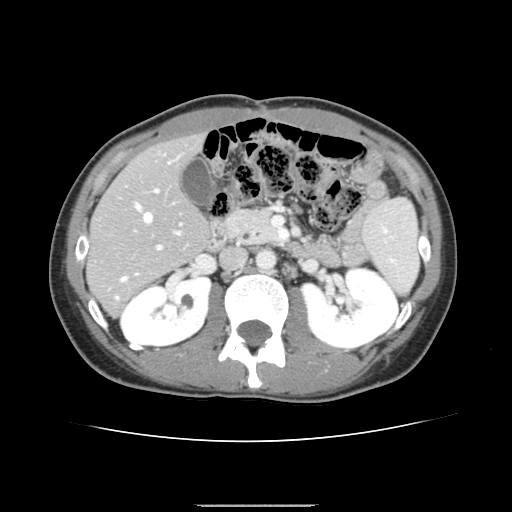
Contrast-enhanced abdominal CT, one axial slice; position 73 of 150 along the scan axis; 120 kVp; soft-tissue window (W 400 / L 40 HU); 2.5 mm slice thickness; 512 × 512 image matrix, field of view 324 × 324 mm. Female patient, age 32 years. From the clinical record (not read from this slice): diagnosis: colorectal cancer liver metastases, imaged before liver resection; multiple liver metastases: yes; largest metastasis: 0.7 cm; disease in both lobes: no.
Outlined on this slice (outlined manually by an expert reader):
- hepatic veins: bounding box <121,203,179,281> (left, top, right, bottom; pixels)
- liver: <88,136,208,314>
- planned liver remnant (the part of the liver to remain after resection): <88,136,209,283>
- portal vein (with intrahepatic branches): <115,157,178,300>